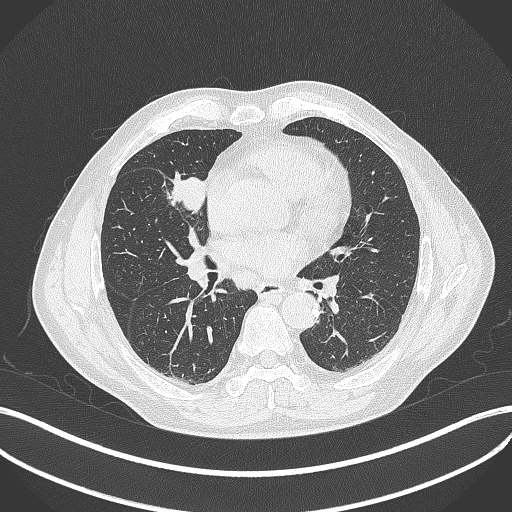
Chest CT, one axial slice. Slice 198 of 429 in the series (ordered by position). Reconstruction kernel B70f. 120 kVp. Lung window (W 1500 / L -600 HU). 1 mm slice thickness. 512 × 512 image matrix, field of view 400 × 400 mm. Male patient, age 61 years. From the clinical record (not read from this slice): clinical TNM (as recorded): T2b N1 M0.
Outlined on this slice (bounding box drawn by a radiologist):
- lung tumour (recorded histology: squamous cell carcinoma): bounding box <167,165,210,218> (left, top, right, bottom; pixels)